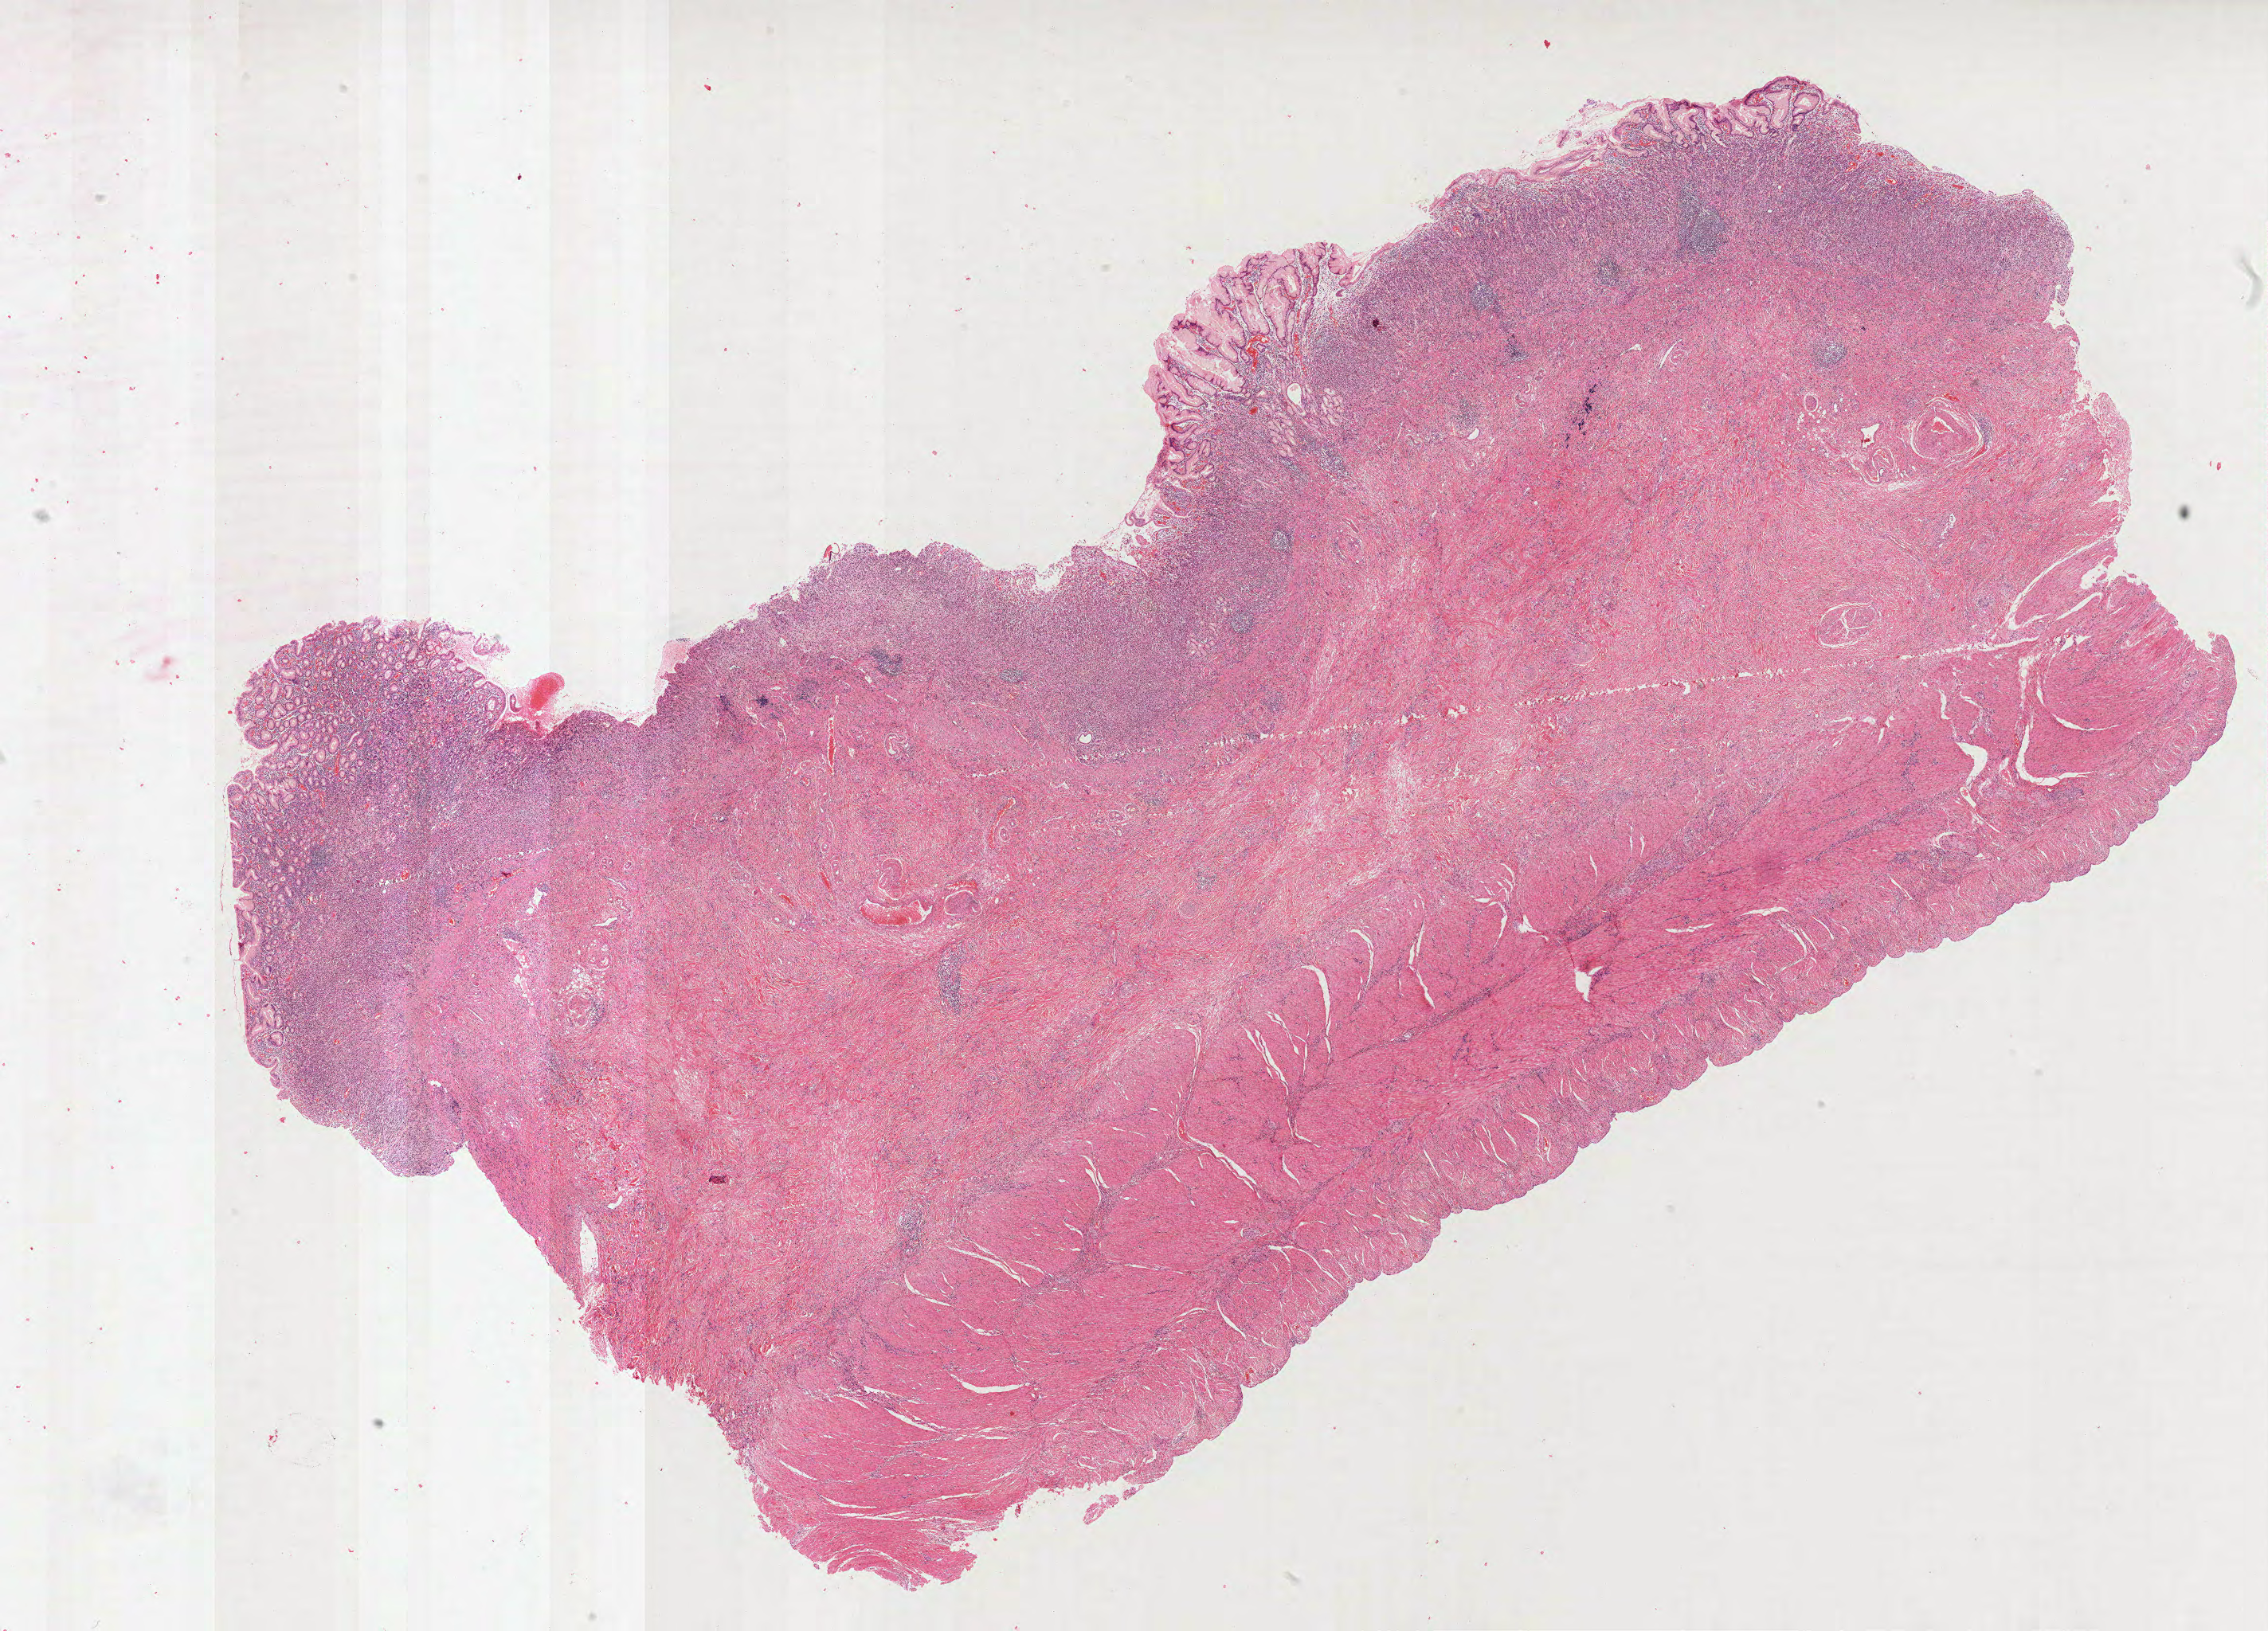
Digitized H&E tissue section (whole slide) — shown as a low-resolution overview of the whole scanned area (about 23.0 x 16.5 mm), formalin-fixed paraffin-embedded (FFPE) diagnostic section, primary tumour sample from the stomach. Patient: female, age at initial diagnosis 70 years.
Diagnosis: Adenocarcinoma, NOS.